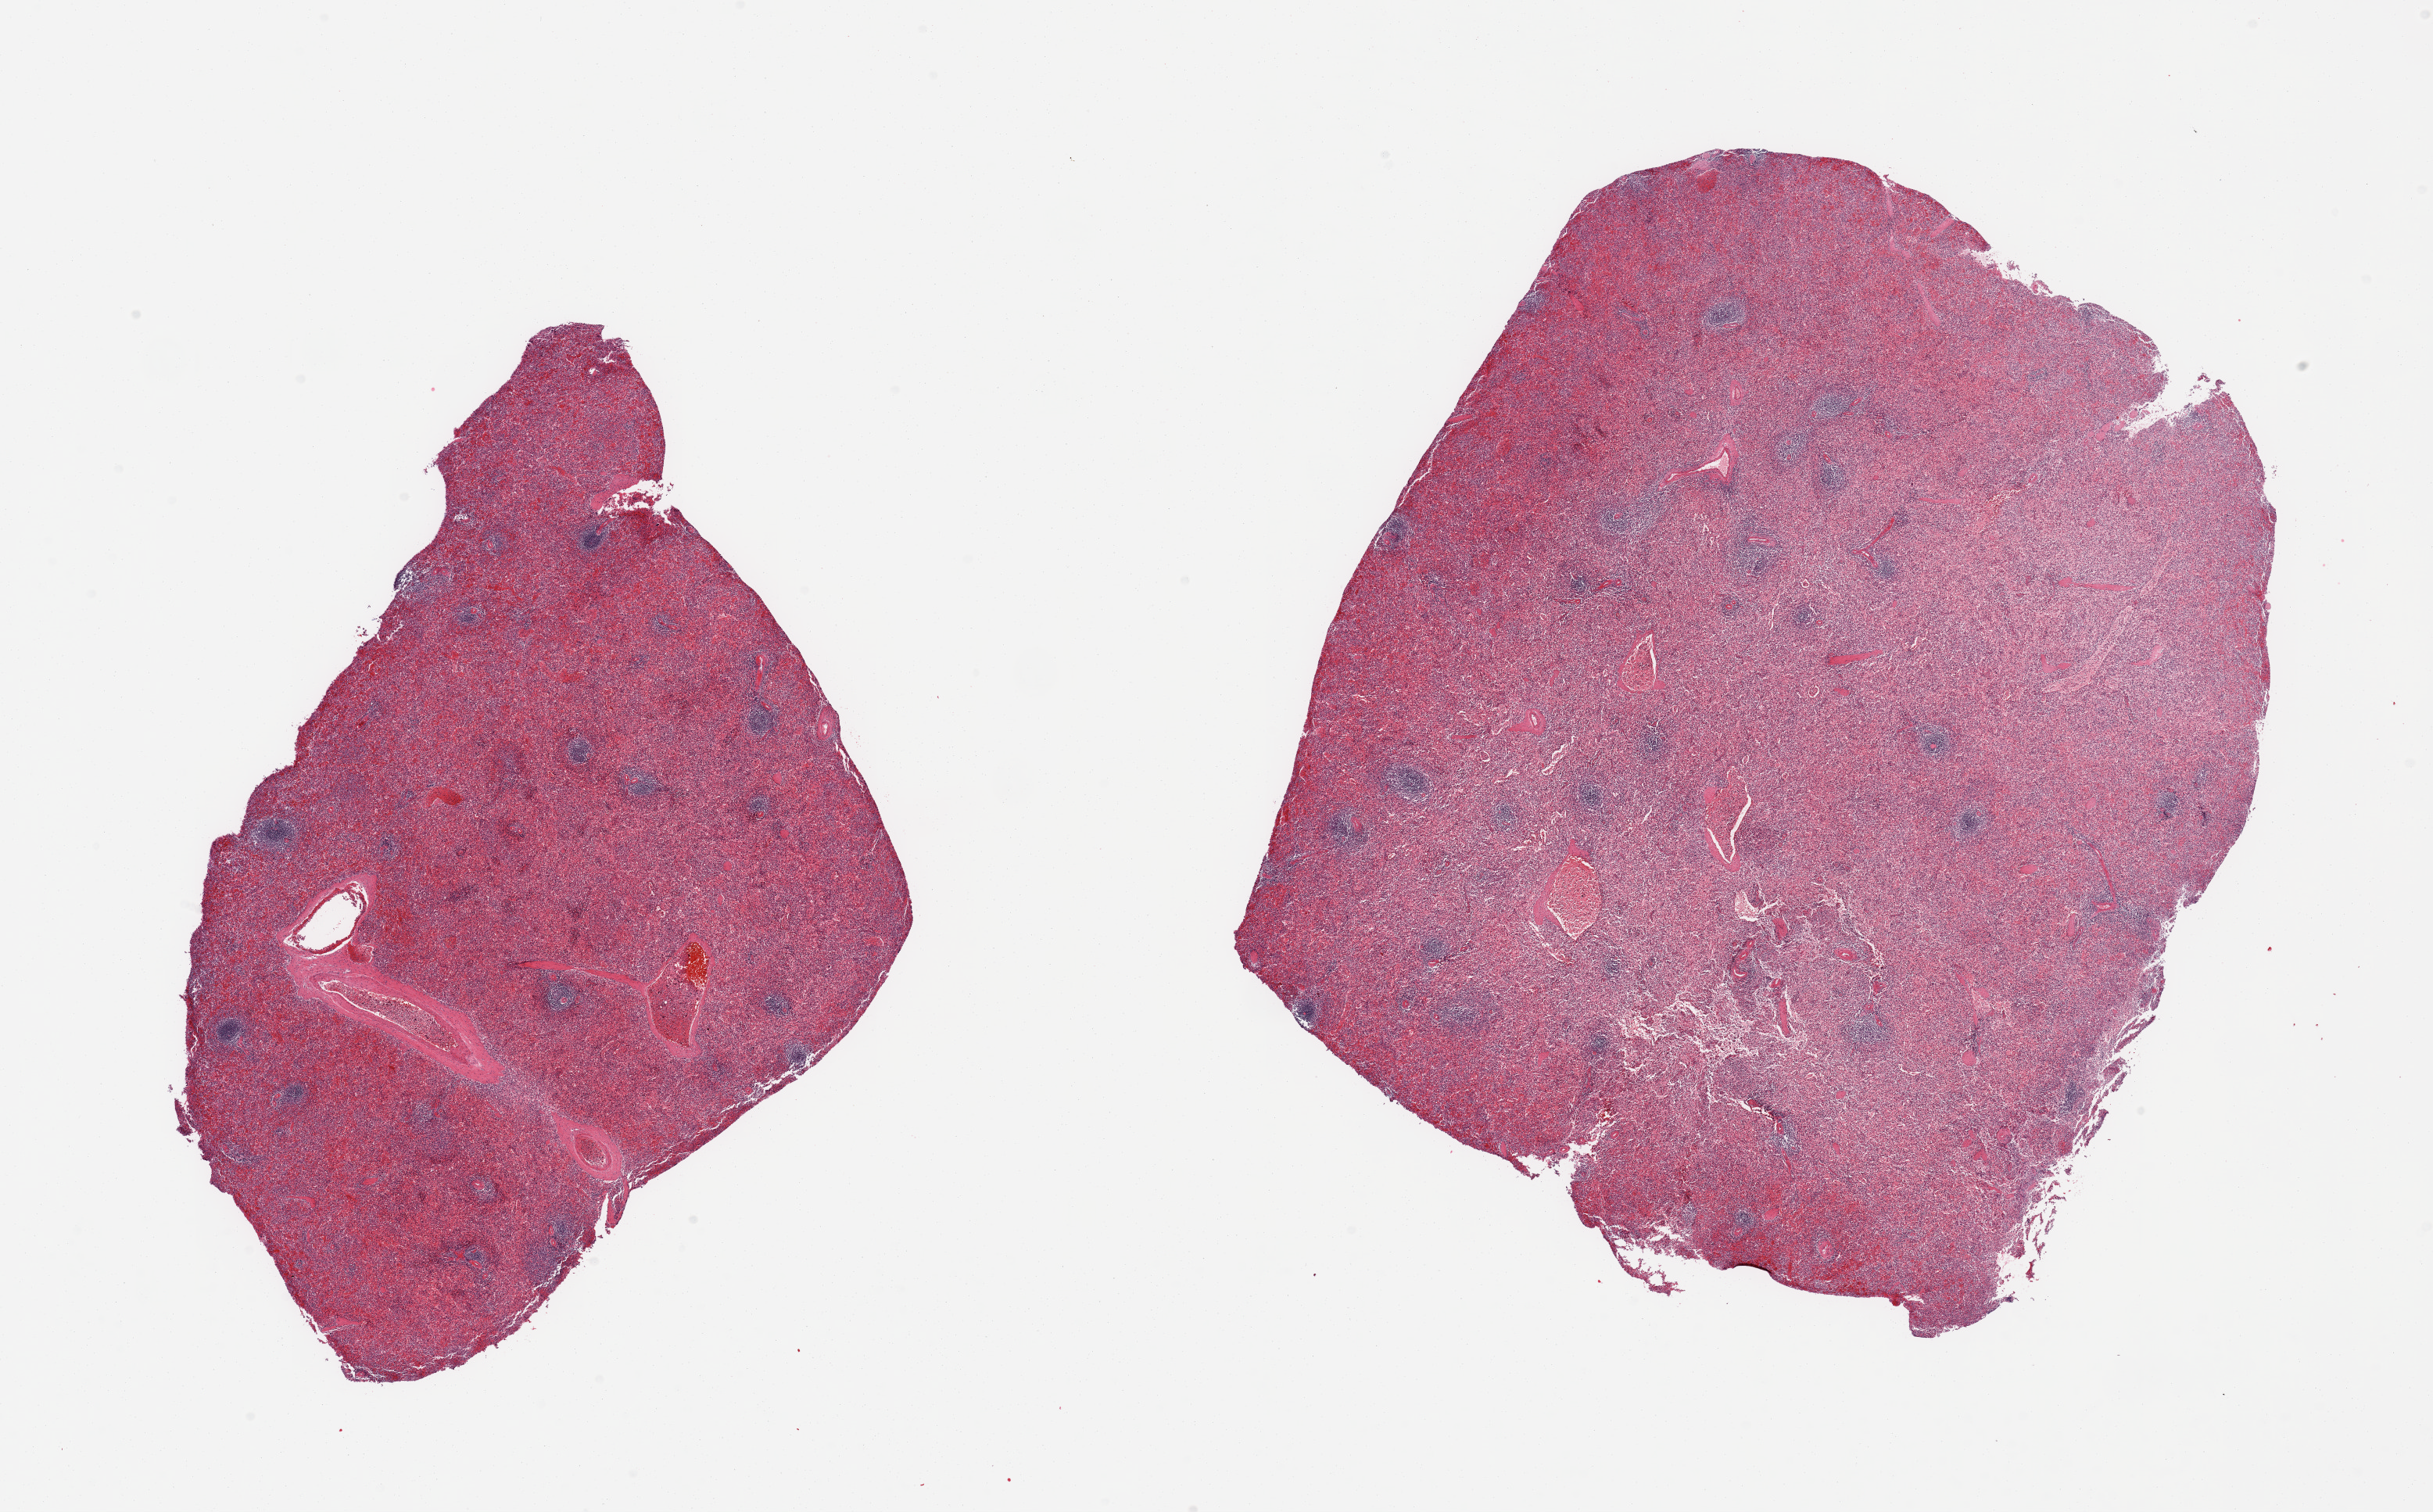
Digitized haematoxylin and eosin-stained section, brightfield, a low-resolution overview of the entire scanned area, about 24.6 x 15.3 mm. PAXgene-fixed, paraffin-embedded tissue. Section of spleen (target tissue). Donor tissue sample. Donor sex: male.
Review note (as recorded): 2 pieces.